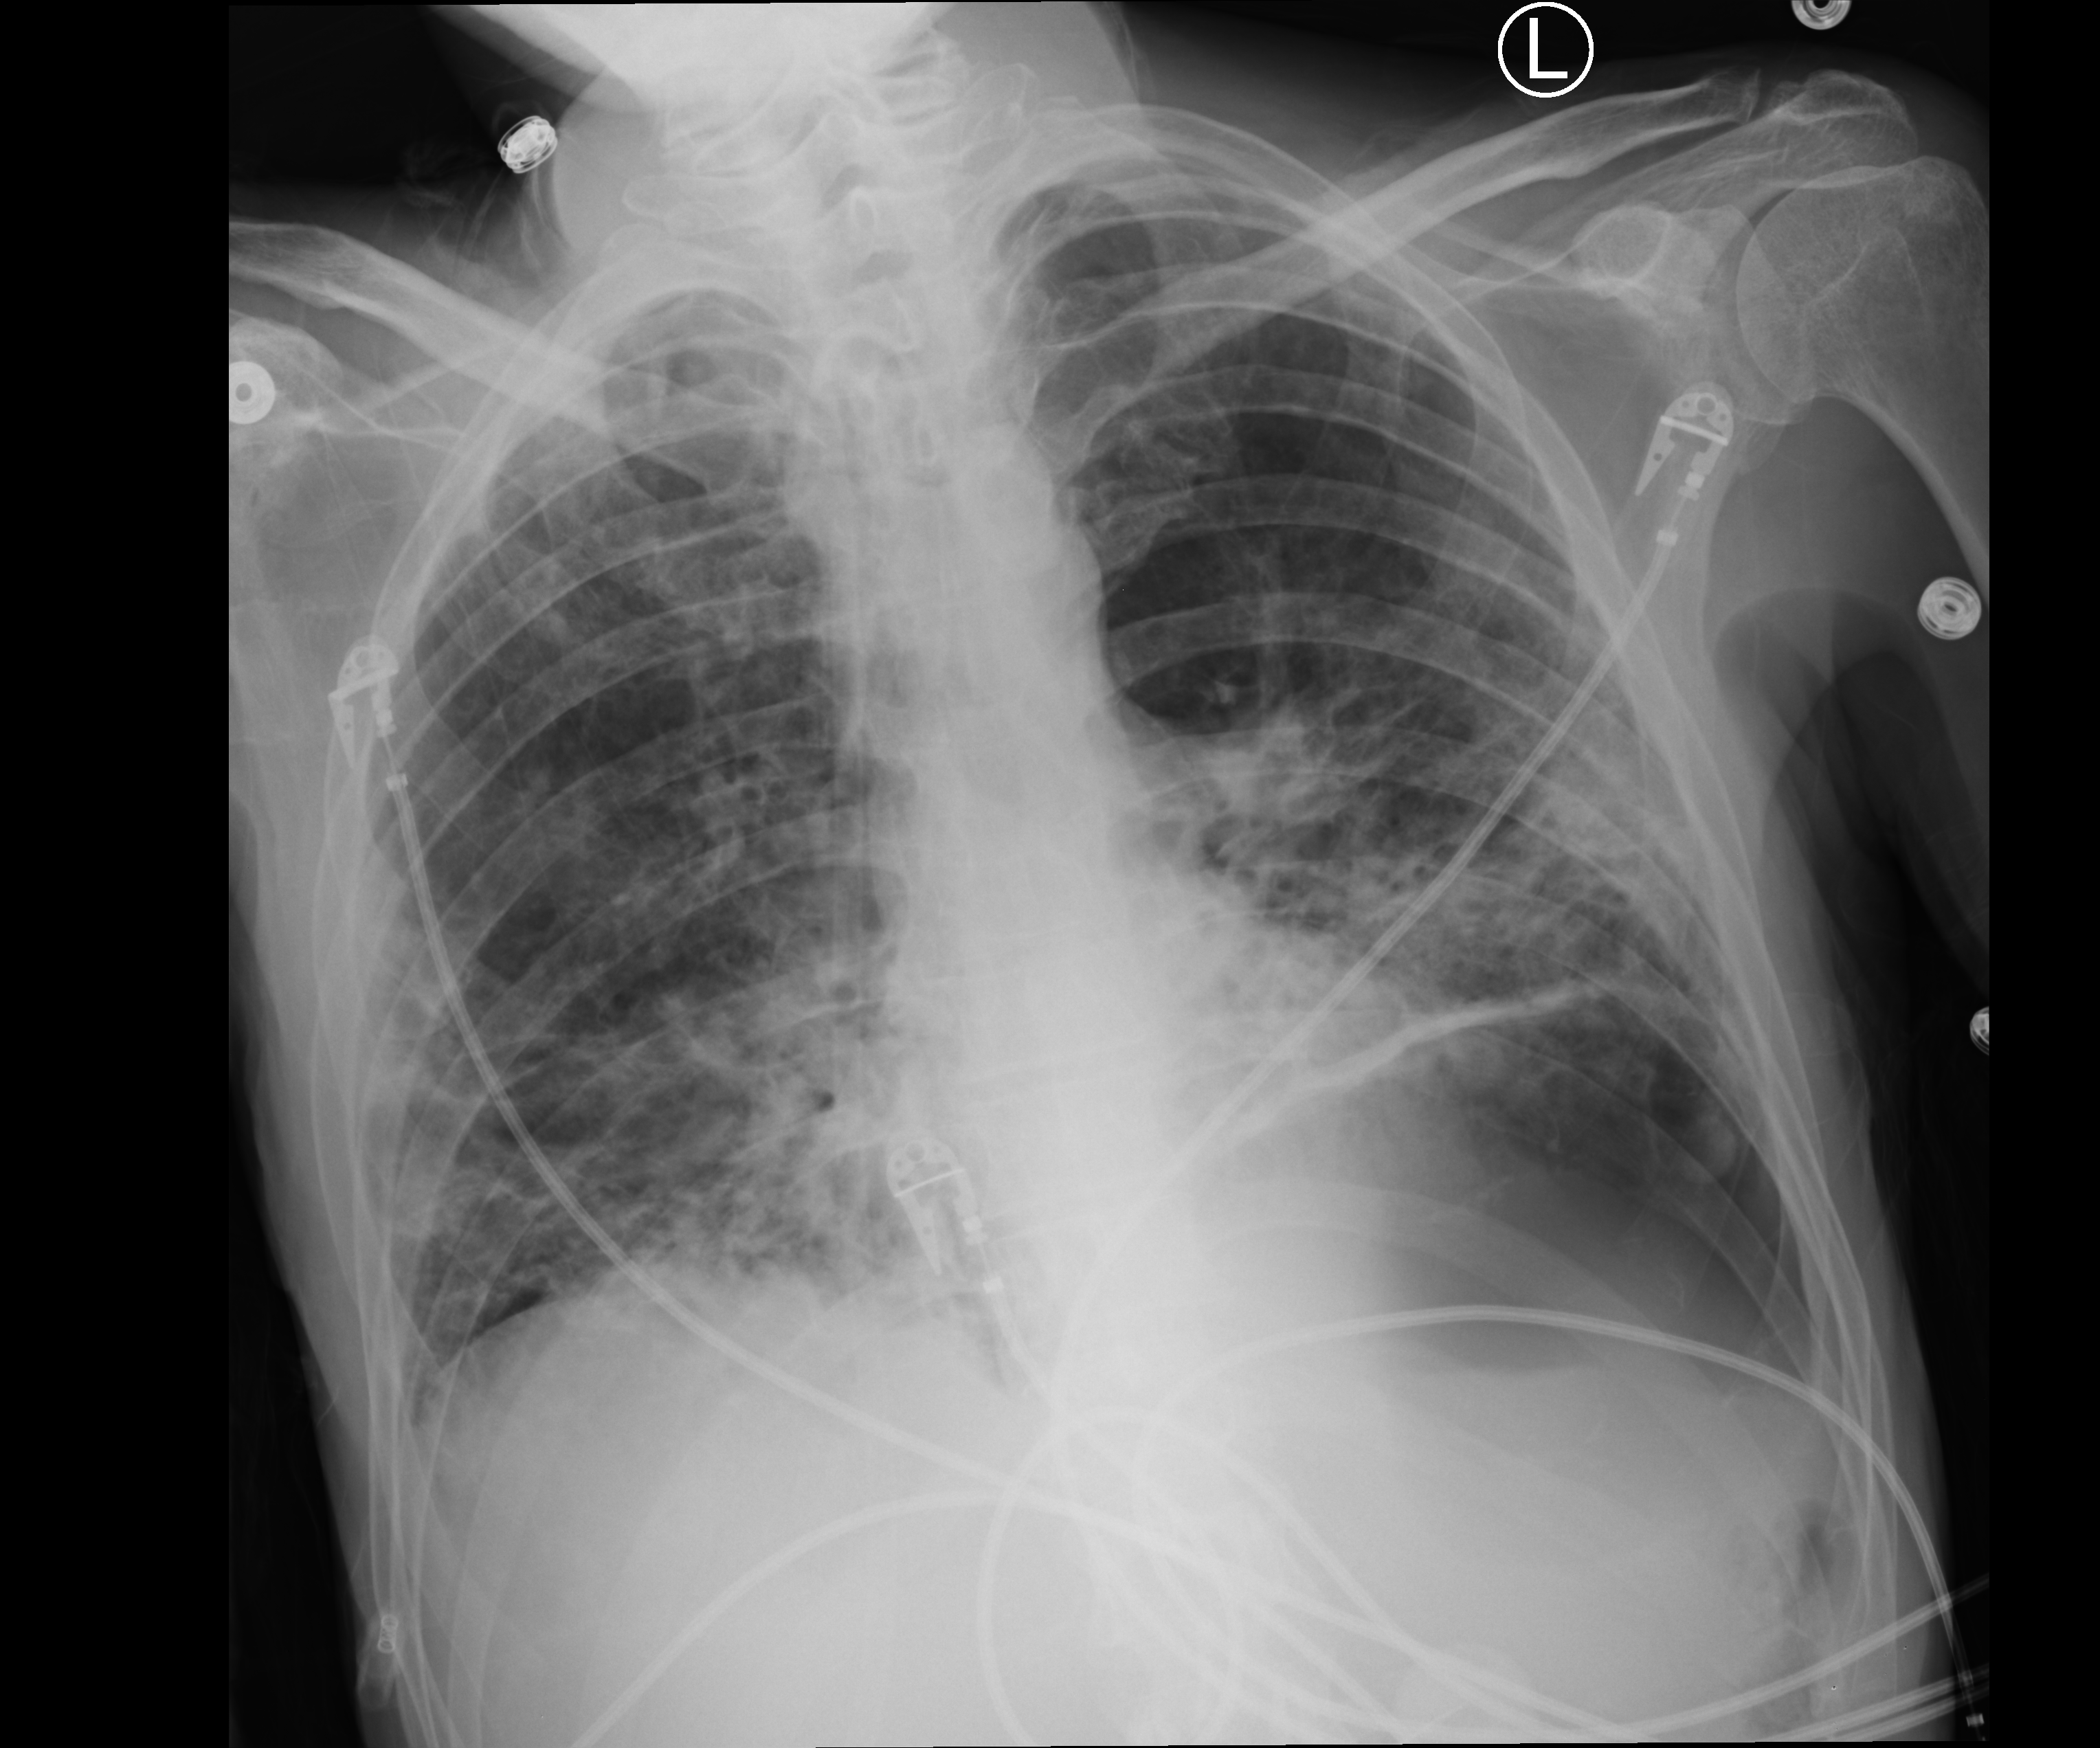
Portable chest radiograph, anteroposterior (AP) projection. Male patient hospitalised with COVID-19, age 18–59 years.
Hospital-stay facts (about this admission, not read from this image; timing relative to this image not recorded): mechanically ventilated during this hospital stay: yes; length of hospital stay: 96 days; admitted to intensive care during this hospital stay: yes.